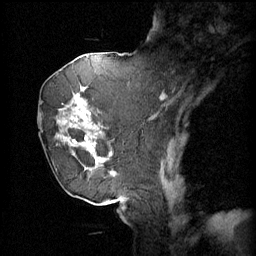
Breast MRI (dynamic contrast-enhanced), one sagittal slice. Position 21 of 60 along the scan axis. 4 images stored at this slice position (order not interpretable as contrast timing). 1.5 T. TE 4.2 ms, TR 11 ms. 2 mm slice thickness. 256 × 256 image matrix, field of view 220 × 220 mm. Female patient, age 72 years.
Annotated regions visible in this slice (semi-automatically segmented with operator editing):
- analysis volume of interest (the breast-tissue region the enhancement analysis was run in; not a lesion): bounding box <45,68,109,163> (left, top, right, bottom; pixels)
- tumour enhancement mask (voxels above the 70 % enhancement threshold inside the analysis volume of interest): <47,68,109,163>